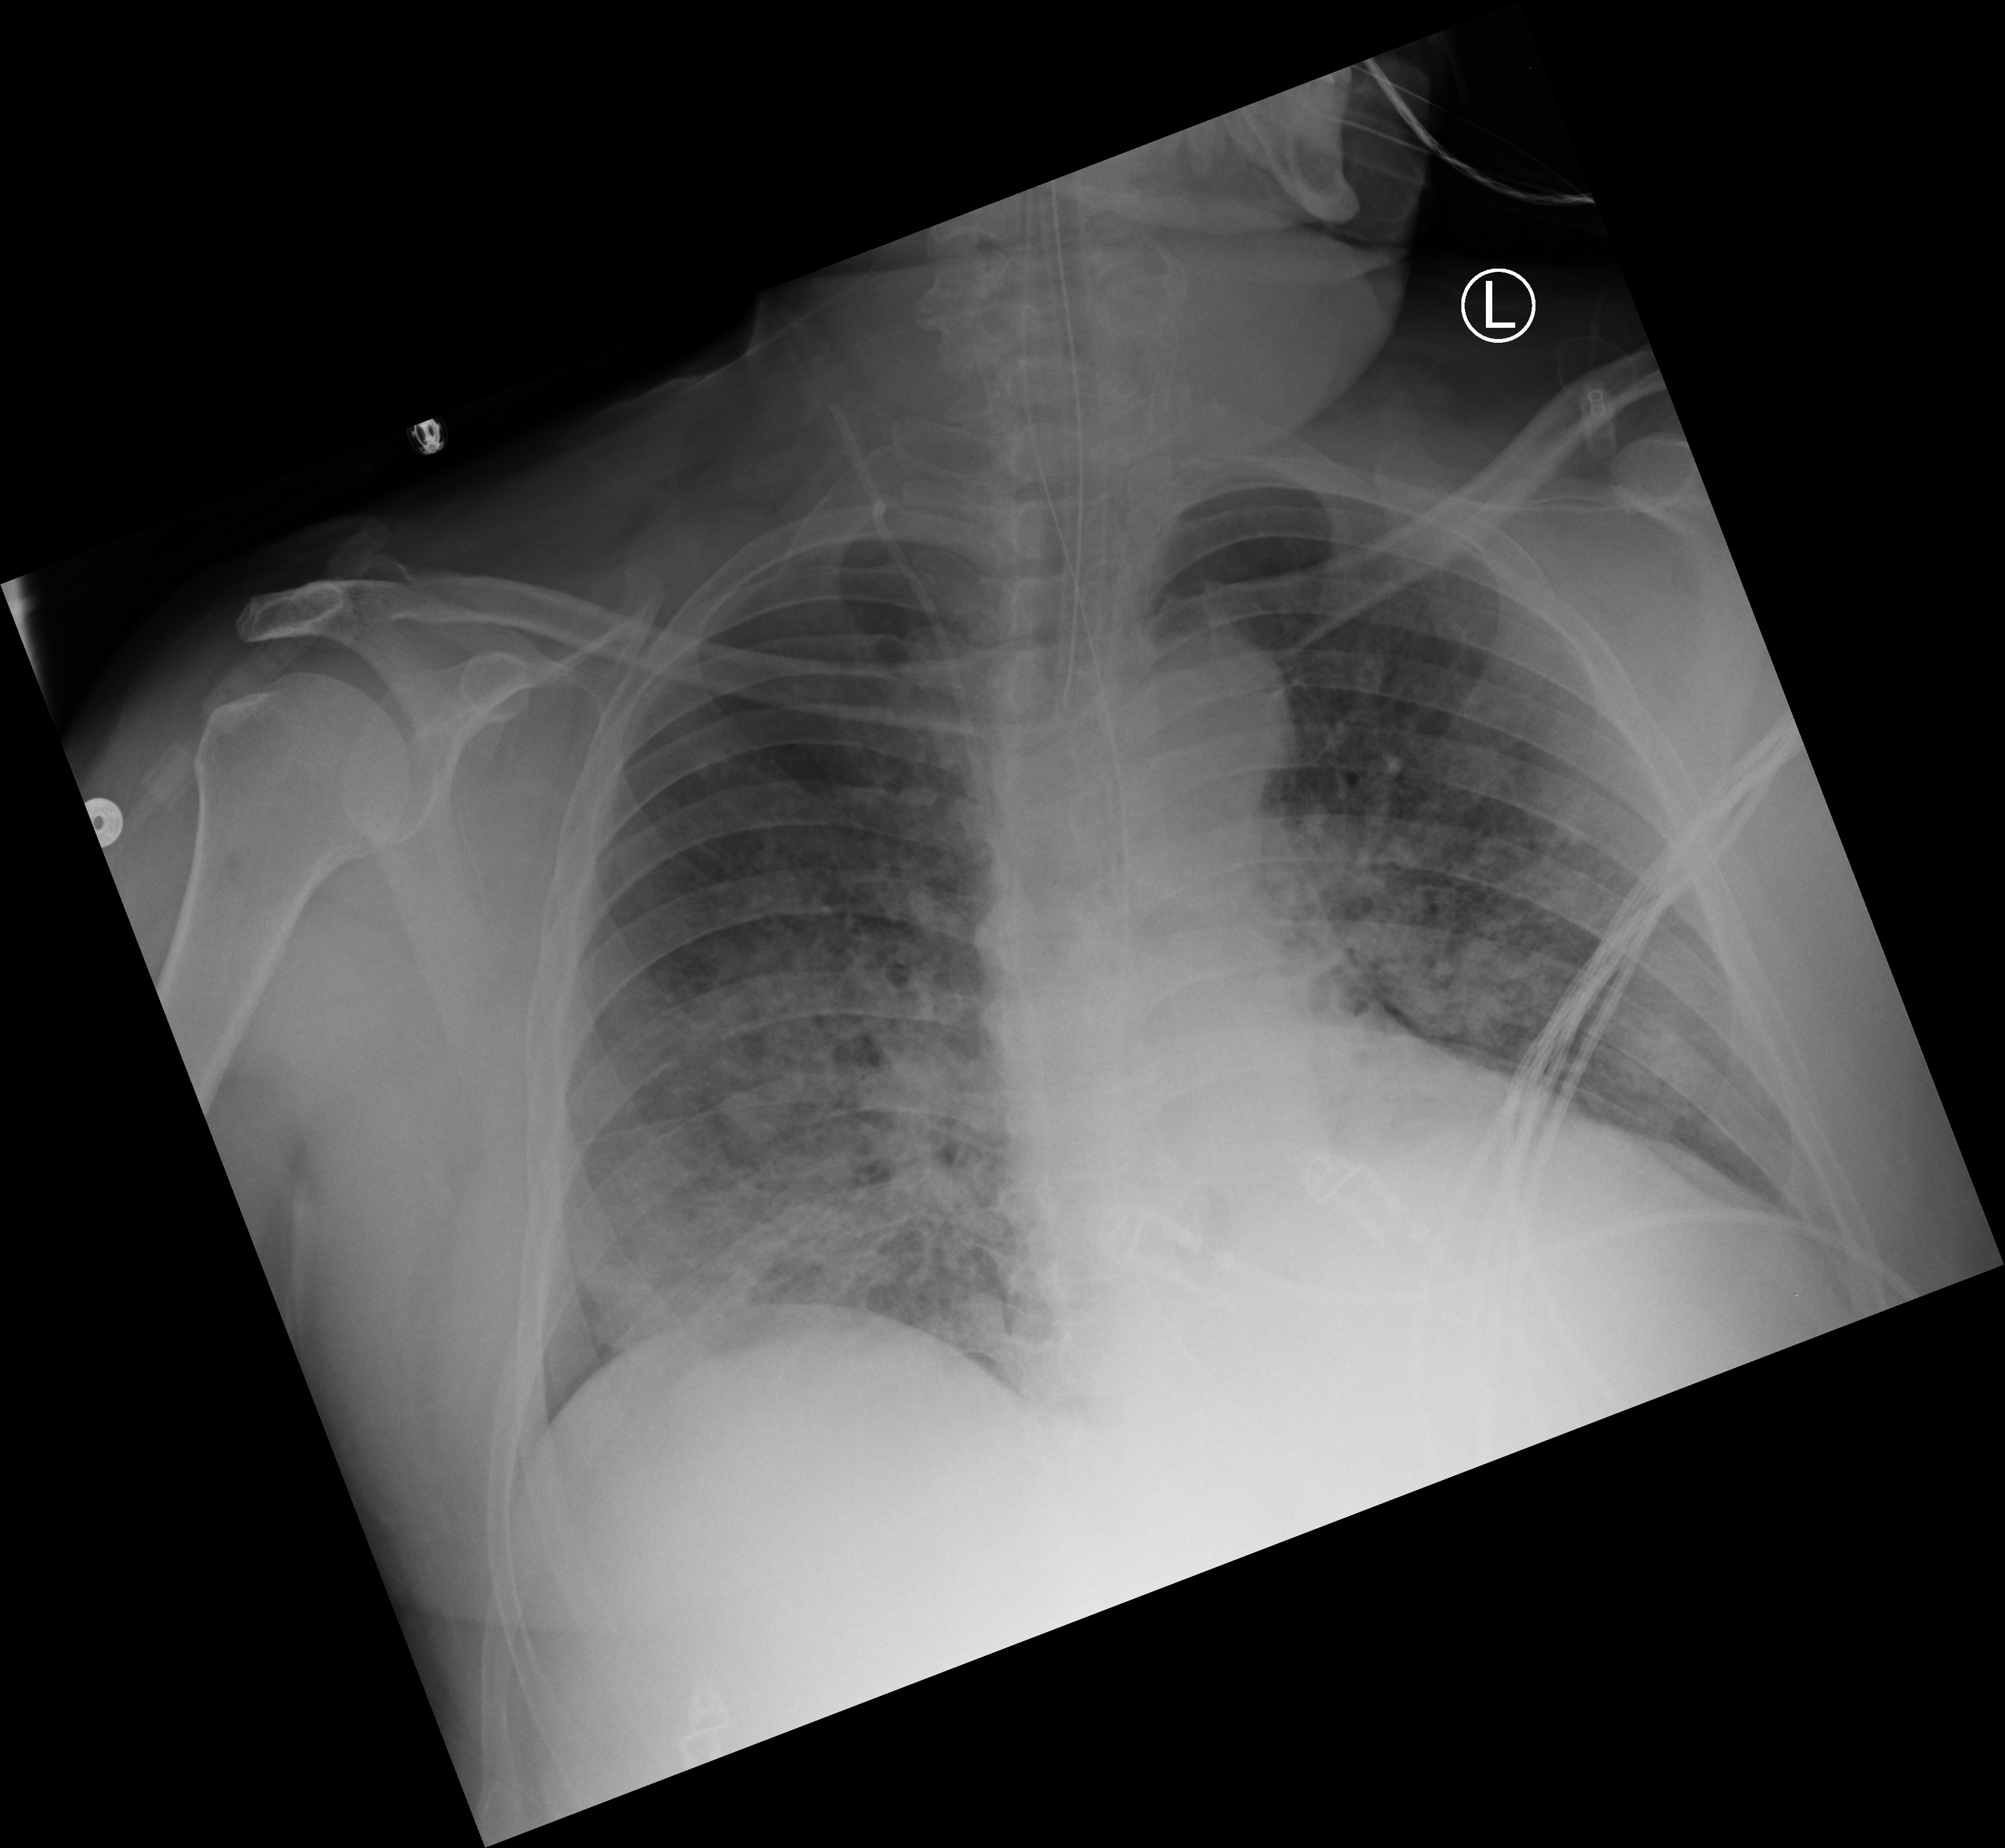
Portable chest radiograph, anteroposterior (AP) projection. Male patient hospitalised with COVID-19, age 60–74 years.
From the hospital-stay record, not from the radiograph (when in the stay this image was taken is not recorded): COPD (admission record): no.